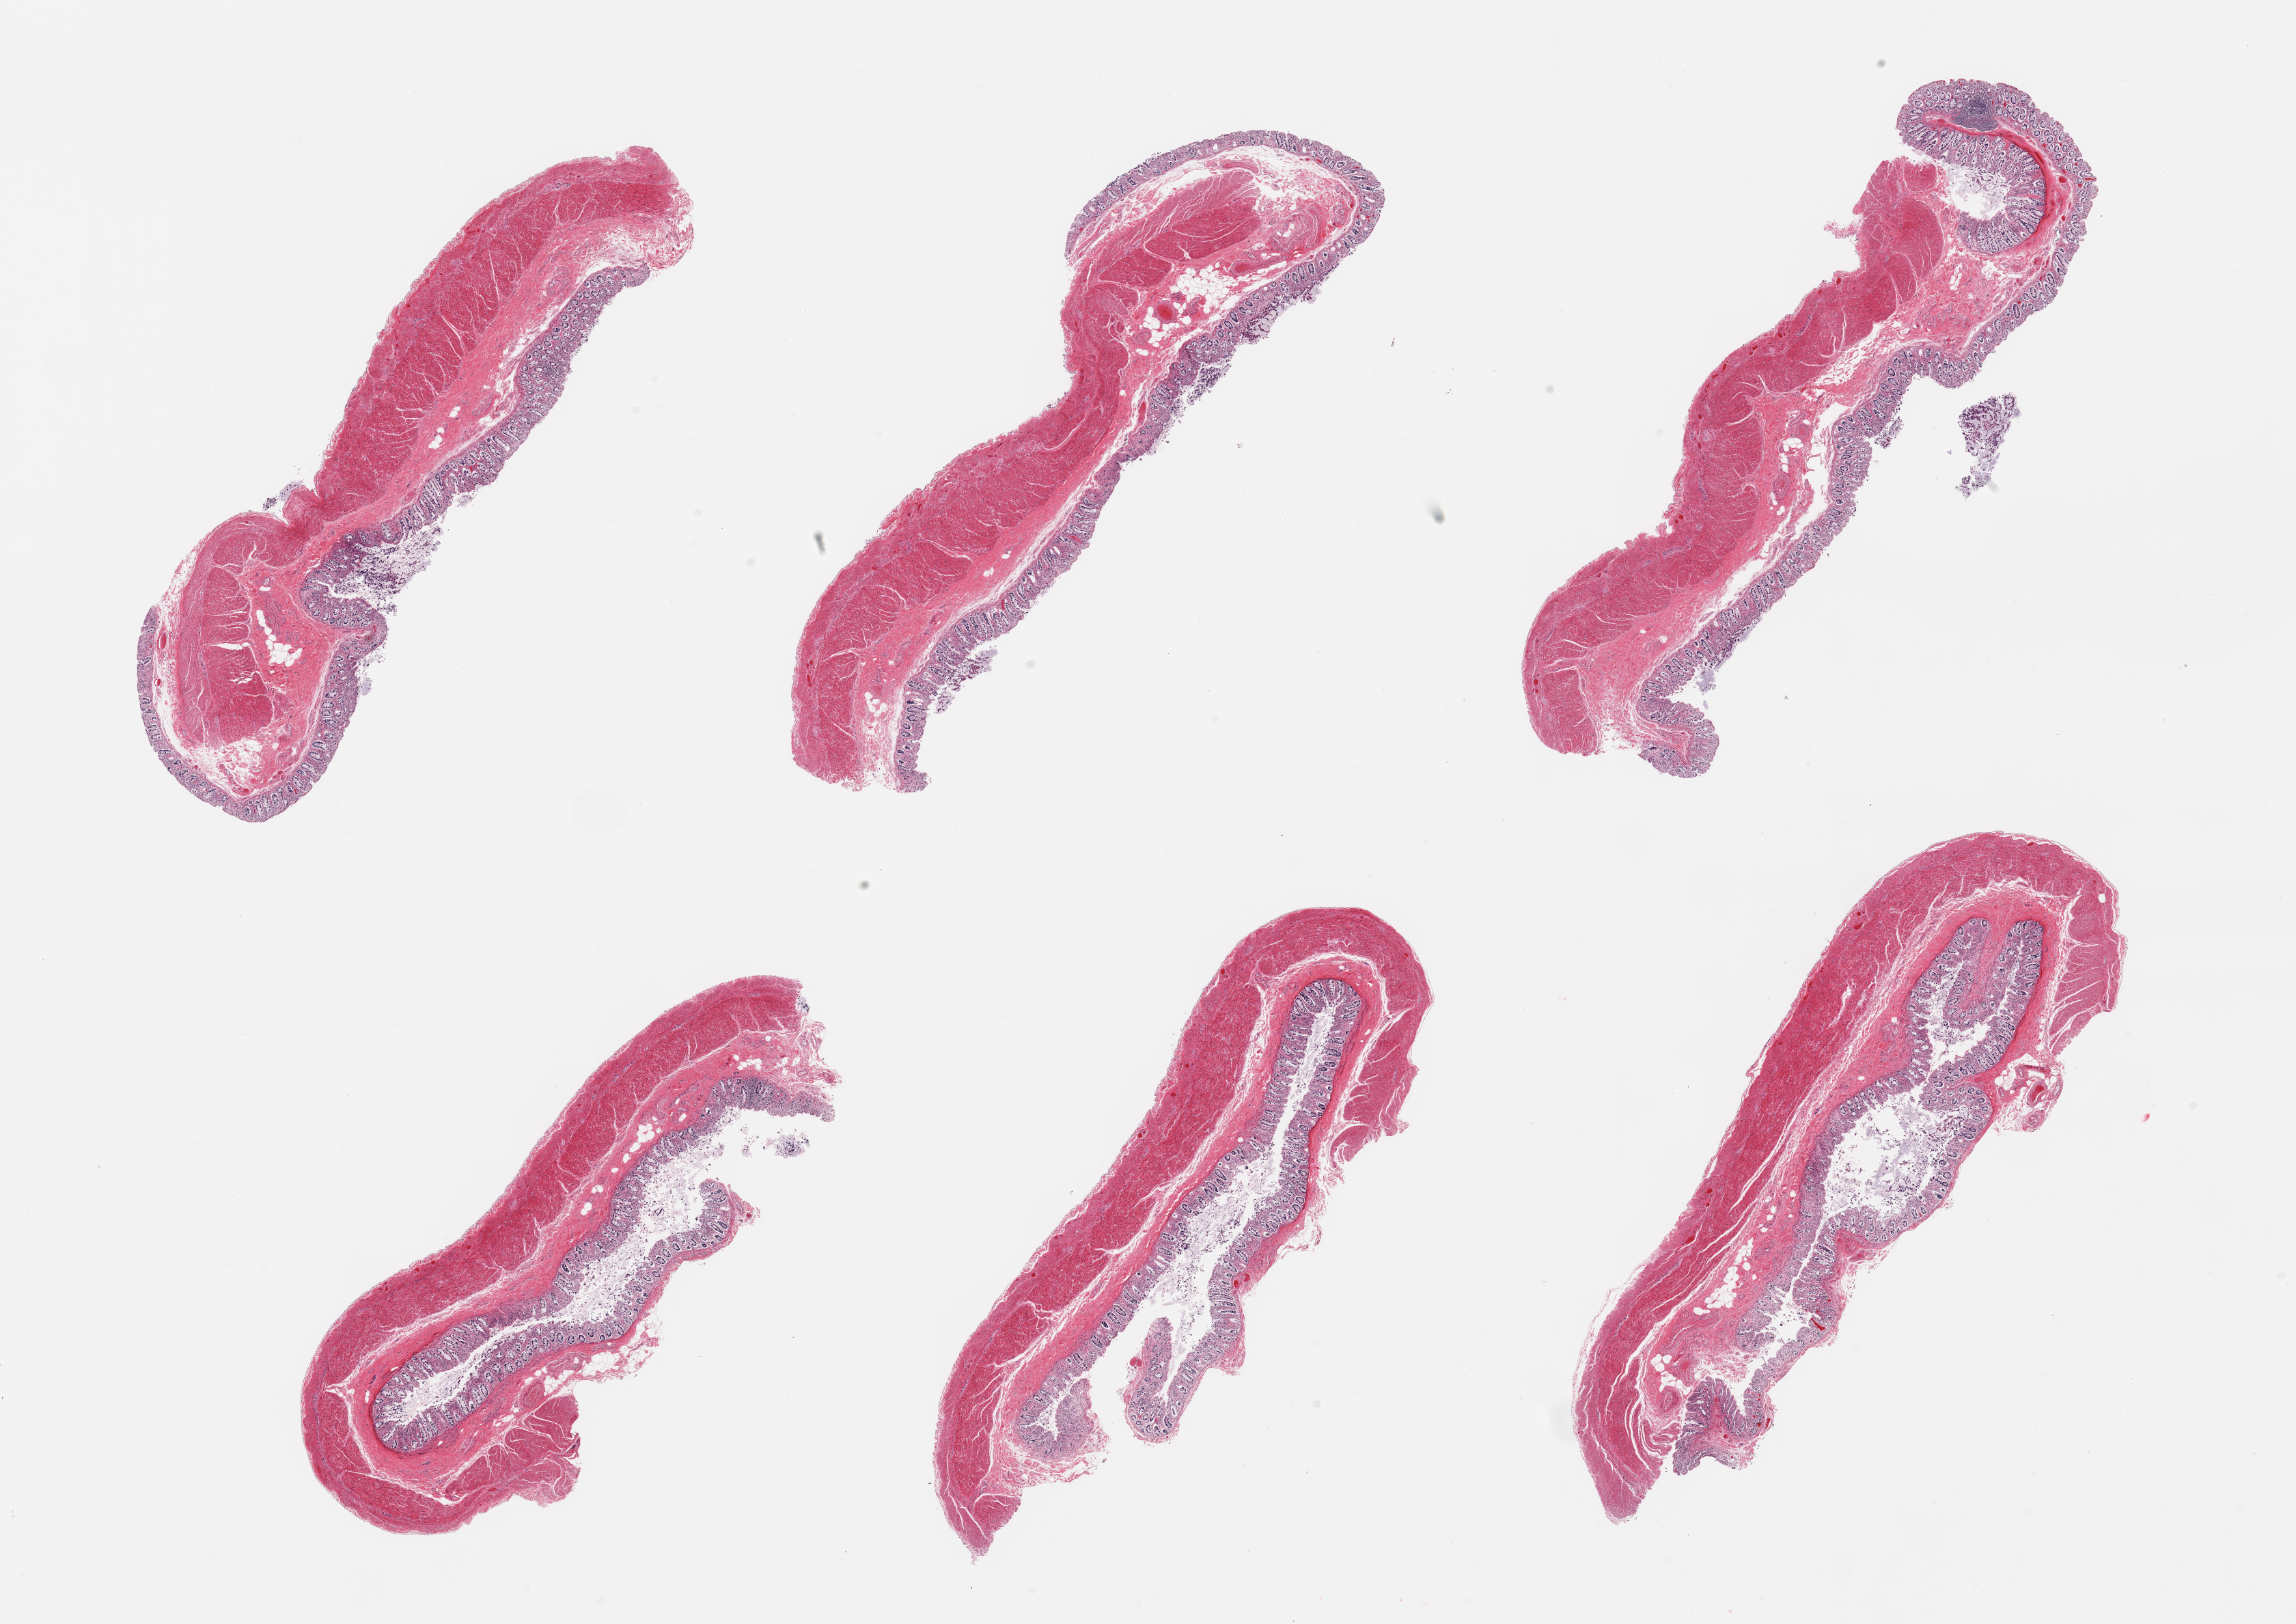
Digitized H&E-stained section — shown as a low-resolution overview of the whole scanned area (about 26.6 x 18.8 mm, acquisition: 20x scan); PAXgene-fixed paraffin-embedded (PFPE) section; section of transverse colon (target tissue); tissue donor sample. Female donor.
Review note (as recorded): 6 pieces; well trimmed; superficial mucosa autolyzed.